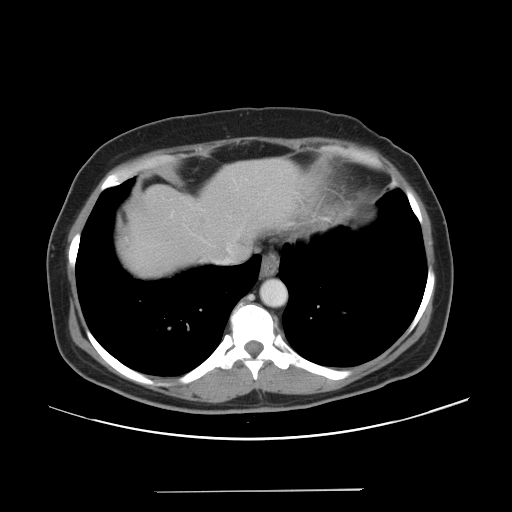
Contrast-enhanced abdominal CT, one axial slice; position 42 of 56 along the scan axis; intravenous contrast given; soft-tissue window (W 400 / L 40 HU); 5 mm slice thickness; 512 × 512 image matrix, field of view 419 × 419 mm. Female patient, age 54 years. Case-level facts recorded for this patient, not image findings: diagnosis: colorectal cancer liver metastases, imaged before liver resection; multiple liver metastases: yes; largest metastasis: 3.2 cm; chemotherapy before resection: yes.
Structures marked on this image (expert manual segmentation):
- hepatic veins: box from (x=222, y=246) to (x=232, y=263) px
- liver: (x=124, y=158)–(x=302, y=276)
- planned liver remnant (the part of the liver to remain after resection): (x=209, y=158)–(x=304, y=248)
- liver metastasis: (x=123, y=229)–(x=131, y=243)